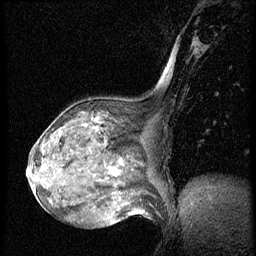
Breast MRI (dynamic contrast-enhanced), one sagittal slice. Position 29 of 56 along the scan axis. Dynamic contrast-enhanced series, image 2 of 3 at this slice position (ordered by acquisition). 1.5 T. TE 4.2 ms, TR 20.4 ms. 256 × 256 image matrix, field of view 200 × 200 mm. Patient: female, 64 years. From the clinical record (not read from this slice): setting: breast cancer imaged before/during neoadjuvant chemotherapy; receptor status: HR-positive, HER2-negative.
Structures marked on this image (semi-automatically segmented with operator editing):
- analysis volume of interest (the breast-tissue region the enhancement analysis was run in; not a lesion): bounding box (x1, y1, x2, y2) in pixels: (48, 101, 139, 186)
- tumour enhancement mask (voxels above the 70 % enhancement threshold inside the analysis volume of interest): (94, 117, 123, 176)